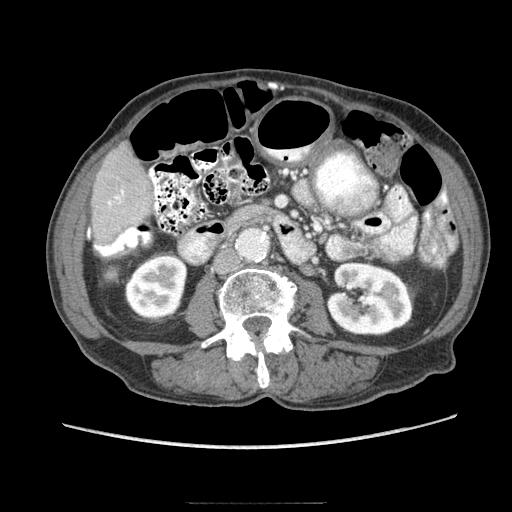
Contrast-enhanced abdominal CT (liver protocol), one axial slice. Position 19 of 83 along the scan axis. Reconstruction kernel STANDARD. Soft-tissue window (W 400 / L 40 HU). 2.5 mm slice thickness. 512 × 512 image matrix. From the clinical record (not read from this slice): diagnosis: hepatocellular carcinoma (patient treated with transarterial chemoembolisation; whether this scan precedes or follows treatment is not stated here); TNM stage (as recorded): Stage-I; Child-Pugh class: A; tumour differentiation: moderately differentiated; tumour nodularity: uninodular.
Structures marked on this image (semi-automatically segmented with operator editing):
- liver parenchyma outside the tumour (the mass and vessels are separate outlines, so this box may not span the whole liver): bounding box (x1, y1, x2, y2) in pixels: (92, 144, 152, 250)
- liver vessels: (96, 190, 124, 249)